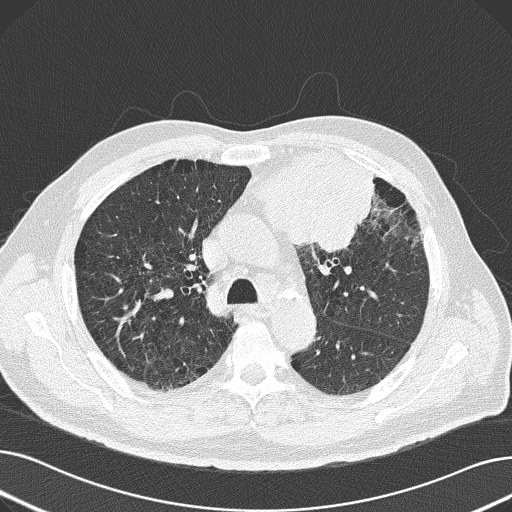
Low-dose screening chest CT, axial slice; baseline annual screen; lung window (W 1500 / L -600 HU); 2 mm slice thickness; lung (sharp) reconstruction kernel (B50f); slice 61 of 165 in the series. Male participant, aged 69 years at enrolment. Former smoker at enrolment.
• Expert-annotated lung lesion, bounding box <229,144,381,253> (left, top, right, bottom; pixels).
• Reader record for this screening exam (exam-level; its link to the box is not recorded): non-calcified nodule or mass ≥4 mm, left upper lobe, 6 × 10 mm, spiculated (stellate) margins, soft tissue attenuation.
• Official screen result: positive, change unspecified: nodule(s) >= 4 mm or enlarging nodule(s), mass(es), or other non-specific abnormalities suspicious for lung cancer.
• Lung cancer was diagnosed 20 days after this screen: non-small cell carcinoma, left upper lobe, poorly differentiated (G3), stage IB (AJCC 6th edition), 100 mm at pathology.